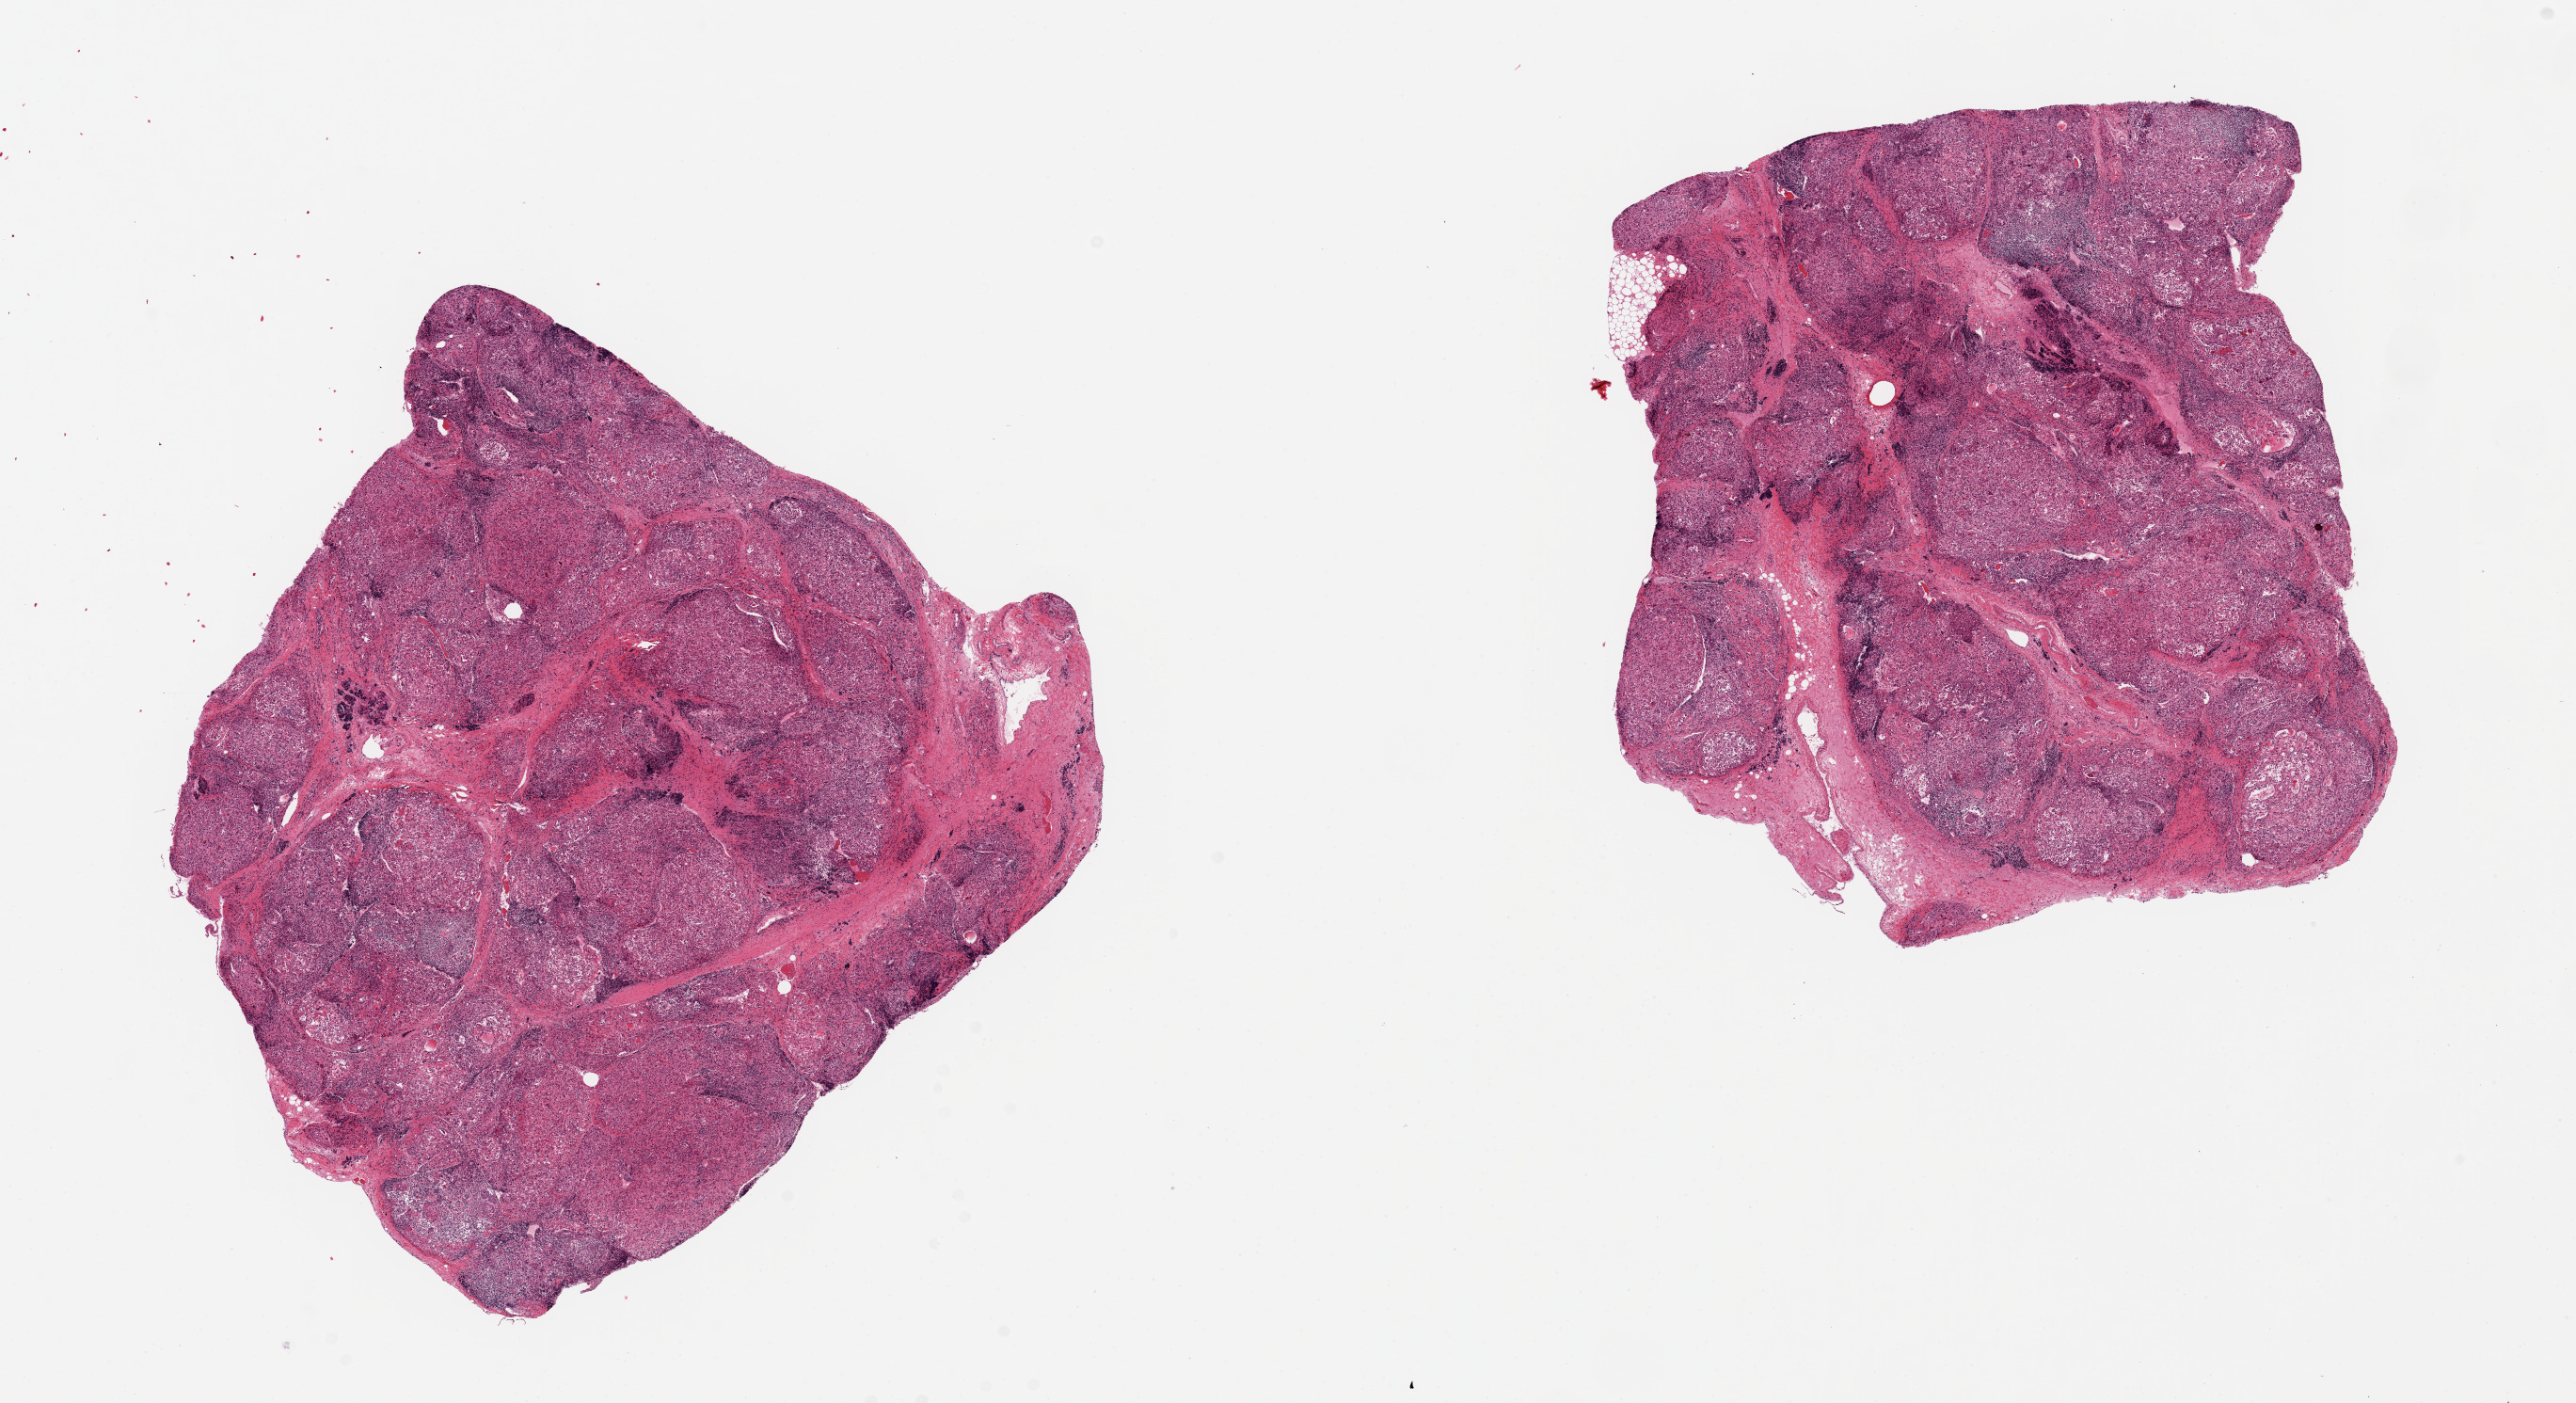
Digitized hematoxylin and eosin (H&E)-stained section, a low-resolution overview of the entire scanned area, about 21.7 x 11.8 mm (acquisition: 20x scan); PAXgene-fixed paraffin-embedded (PFPE) section; section of thyroid (target tissue); tissue donor sample. Male donor.
Reviewer comment on this tissue sample: 2 pieces, 7x6 & 7x6mm; unusually badly autolyzed, diffuse Hashimoto thyroiditis with regressive changes.